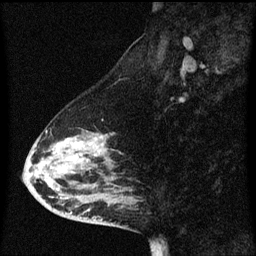
Breast MRI (dynamic contrast-enhanced), one sagittal slice; slice 27 of 60 in the series (ordered by position); dynamic contrast-enhanced series, image 2 of 3 at this slice position (ordered by acquisition); 1.5 T; TE 4.2 ms, TR 8.4 ms; 2 mm slice thickness; 256 × 256 image matrix, field of view 200 × 200 mm. Patient: female, 47 years. Case-level facts recorded for this patient, not image findings: setting: breast cancer imaged before/during neoadjuvant chemotherapy; receptor status: HER2-positive.
Structures marked on this image (semi-automatic segmentation, software-assisted and operator-edited):
- analysis volume of interest (the breast-tissue region the enhancement analysis was run in; not a lesion): bounding box <26,122,137,201> (left, top, right, bottom; pixels)
- tumour enhancement mask (voxels above the 70 % enhancement threshold inside the analysis volume of interest): <59,136,102,161>